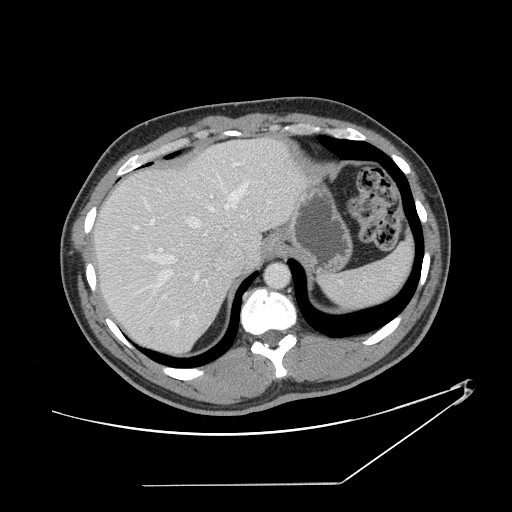
Contrast-enhanced abdominal CT, one axial slice; position 114 of 152 along the scan axis; reconstruction kernel STANDARD; 120 kVp; intravenous contrast given; soft-tissue window (W 400 / L 40 HU); 512 × 512 image matrix, field of view 432 × 432 mm. Male patient, age 45 years. Case-level facts recorded for this patient, not image findings: diagnosis: colorectal cancer liver metastases, imaged before liver resection; multiple liver metastases: no; largest metastasis: 1 cm; disease in both lobes: no.
Structures marked on this image (manually delineated by an expert):
- hepatic veins: bounding box <111,173,250,287> (left, top, right, bottom; pixels)
- liver: <96,138,304,354>
- planned liver remnant (the part of the liver to remain after resection): <96,161,234,355>
- portal vein (with intrahepatic branches): <159,196,212,323>